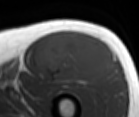
MRI of an extremity soft-tissue mass, one axial slice; slice 56 of 86 in the series (ordered by position); MR volume resampled by the dataset authors to the PET/CT grid (not the native acquisition matrix); 139 × 117 image matrix, field of view 136 × 114 mm. Male patient. From the clinical record (not read from this slice): histological type: extraskeletal osteosarcoma; grade: high; site of the primary tumour: thigh.
Structures marked on this image (expert contour drawn on MRI and transferred to this co-registered scan by the dataset authors):
- gross tumour volume (mass): box from (x=36, y=30) to (x=117, y=83) px